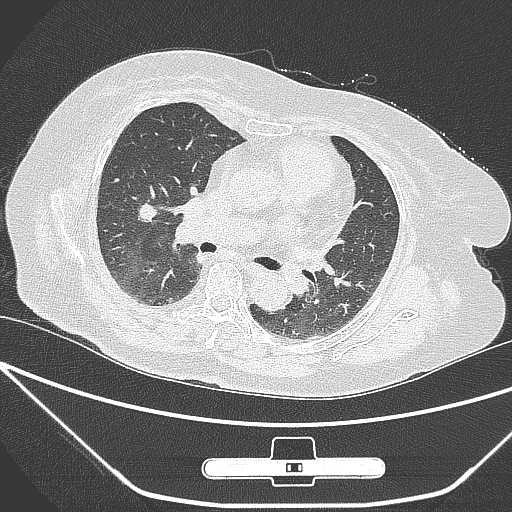
Chest CT, one axial slice; slice 154 of 245 in the series (ordered by position); 120 kVp; lung window (W 1500 / L -600 HU); 1 mm slice thickness; 512 × 512 image matrix, field of view 365 × 365 mm. Female patient, age 65 years. Case-level facts recorded for this patient, not image findings: clinical TNM (as recorded): T1c N0 M0; histopathological grade: G3.
Structures marked on this image (rectangle marked by the reading radiologist):
- lung tumour (recorded histology: adenocarcinoma): box from (x=132, y=198) to (x=157, y=231) px